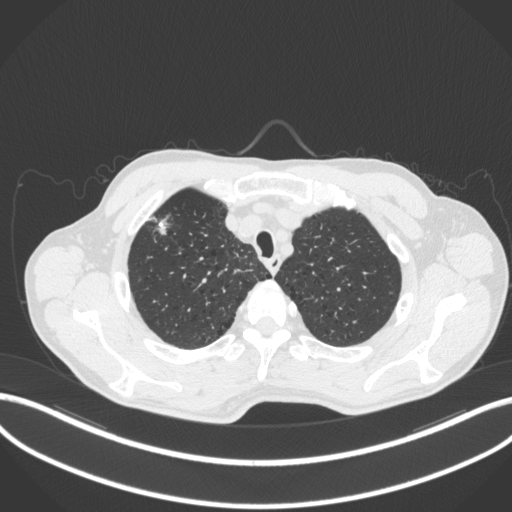
Chest CT, one axial slice. Slice 359 of 414 in the series (ordered by position). Reconstruction kernel B31f. 120 kVp. Lung window (W 1500 / L -600 HU). 512 × 512 image matrix, field of view 400 × 400 mm. Patient: male, 69 years. From the clinical record (not read from this slice): clinical TNM (as recorded): T1b N1 M0.
Annotated regions visible in this slice (rectangle marked by the reading radiologist):
- lung tumour (recorded histology: adenocarcinoma): bounding box <150,214,181,246> (left, top, right, bottom; pixels)